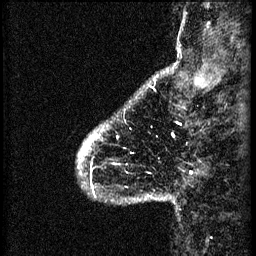
Breast MRI (dynamic contrast-enhanced), one sagittal slice. Position 6 of 60 along the scan axis. 3 images stored at this slice position (order not interpretable as contrast timing). 1.5 T. TE 4.2 ms, TR 8.2 ms. 2.2 mm slice thickness. 256 × 256 image matrix, field of view 180 × 180 mm. Patient: female, 41 years.
Annotated regions visible in this slice (semi-automatically segmented with operator editing):
- analysis volume of interest (the breast-tissue region the enhancement analysis was run in; not a lesion): bounding box (x1, y1, x2, y2) in pixels: (79, 126, 154, 203)
- tumour enhancement mask (voxels above the 70 % enhancement threshold inside the analysis volume of interest): (81, 140, 115, 191)